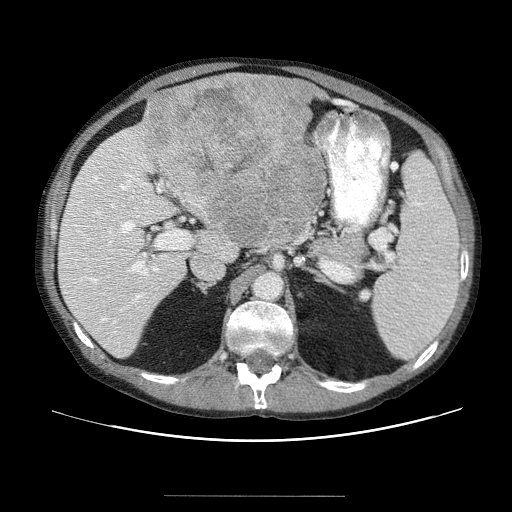
Contrast-enhanced abdominal CT (liver protocol), one axial slice. 120 kVp. Soft-tissue window (W 400 / L 40 HU). 512 × 512 image matrix. Case-level facts recorded for this patient, not image findings: diagnosis: hepatocellular carcinoma (patient treated with transarterial chemoembolisation; whether this scan precedes or follows treatment is not stated here); TNM stage (as recorded): Stage-IVB; Child-Pugh class: B.
Outlined on this slice (semi-automatic segmentation, software-assisted and operator-edited):
- liver parenchyma outside the tumour (the mass and vessels are separate outlines, so this box may not span the whole liver): bounding box [x1, y1, x2, y2] px = [56, 101, 326, 356]
- mass: [135, 74, 329, 253]
- liver vessels: [65, 148, 171, 351]